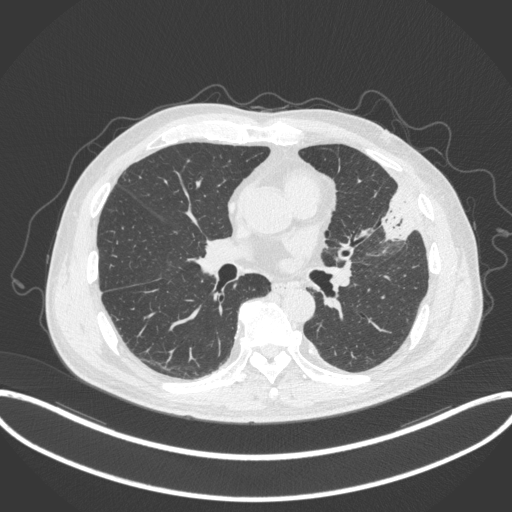
Chest CT, one axial slice; slice 171 of 382 in the series (ordered by position); reconstruction kernel B31f; 120 kVp; lung window (W 1500 / L -600 HU); 1 mm slice thickness; 512 × 512 image matrix, field of view 415 × 415 mm. Patient: male, 64 years. From the clinical record (not read from this slice): clinical TNM (as recorded): T4 N1 M0; histopathological grade: G3.
Outlined on this slice (rectangle marked by the reading radiologist):
- lung tumour (recorded histology: adenocarcinoma): box from (x=380, y=186) to (x=418, y=246) px